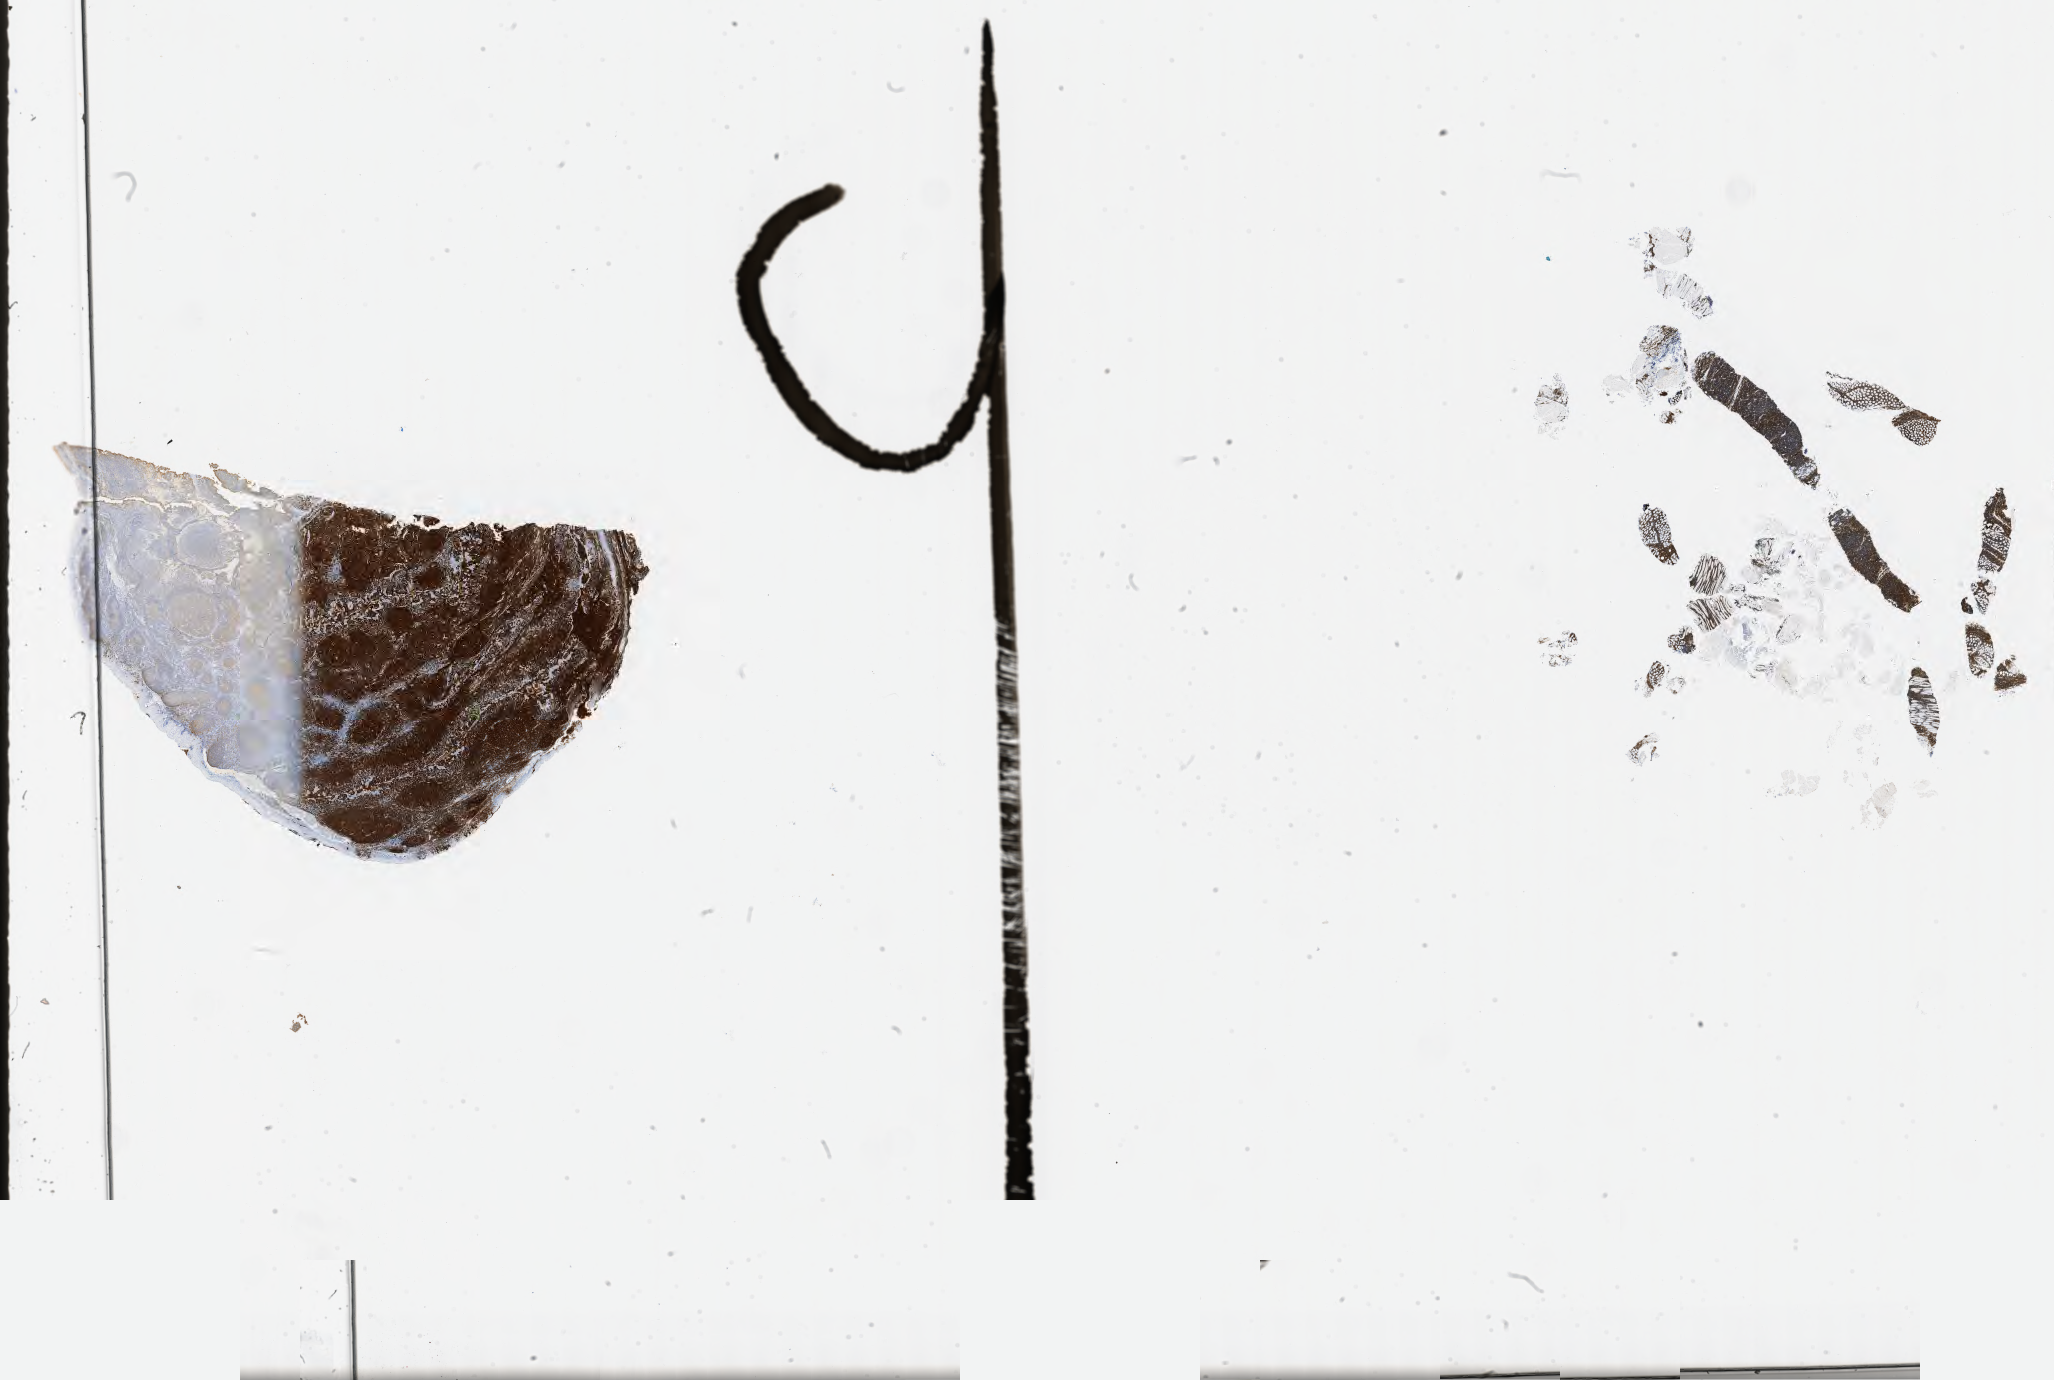
IHC for CD20, whole-slide image, a low-resolution overview of the entire scanned area, about 33.2 x 22.3 mm. Tumor tissue. Anatomic site: retroperitoneum. Patient: female, 53 years old.
Histologic diagnosis: Burkitt lymphoma, NOS.